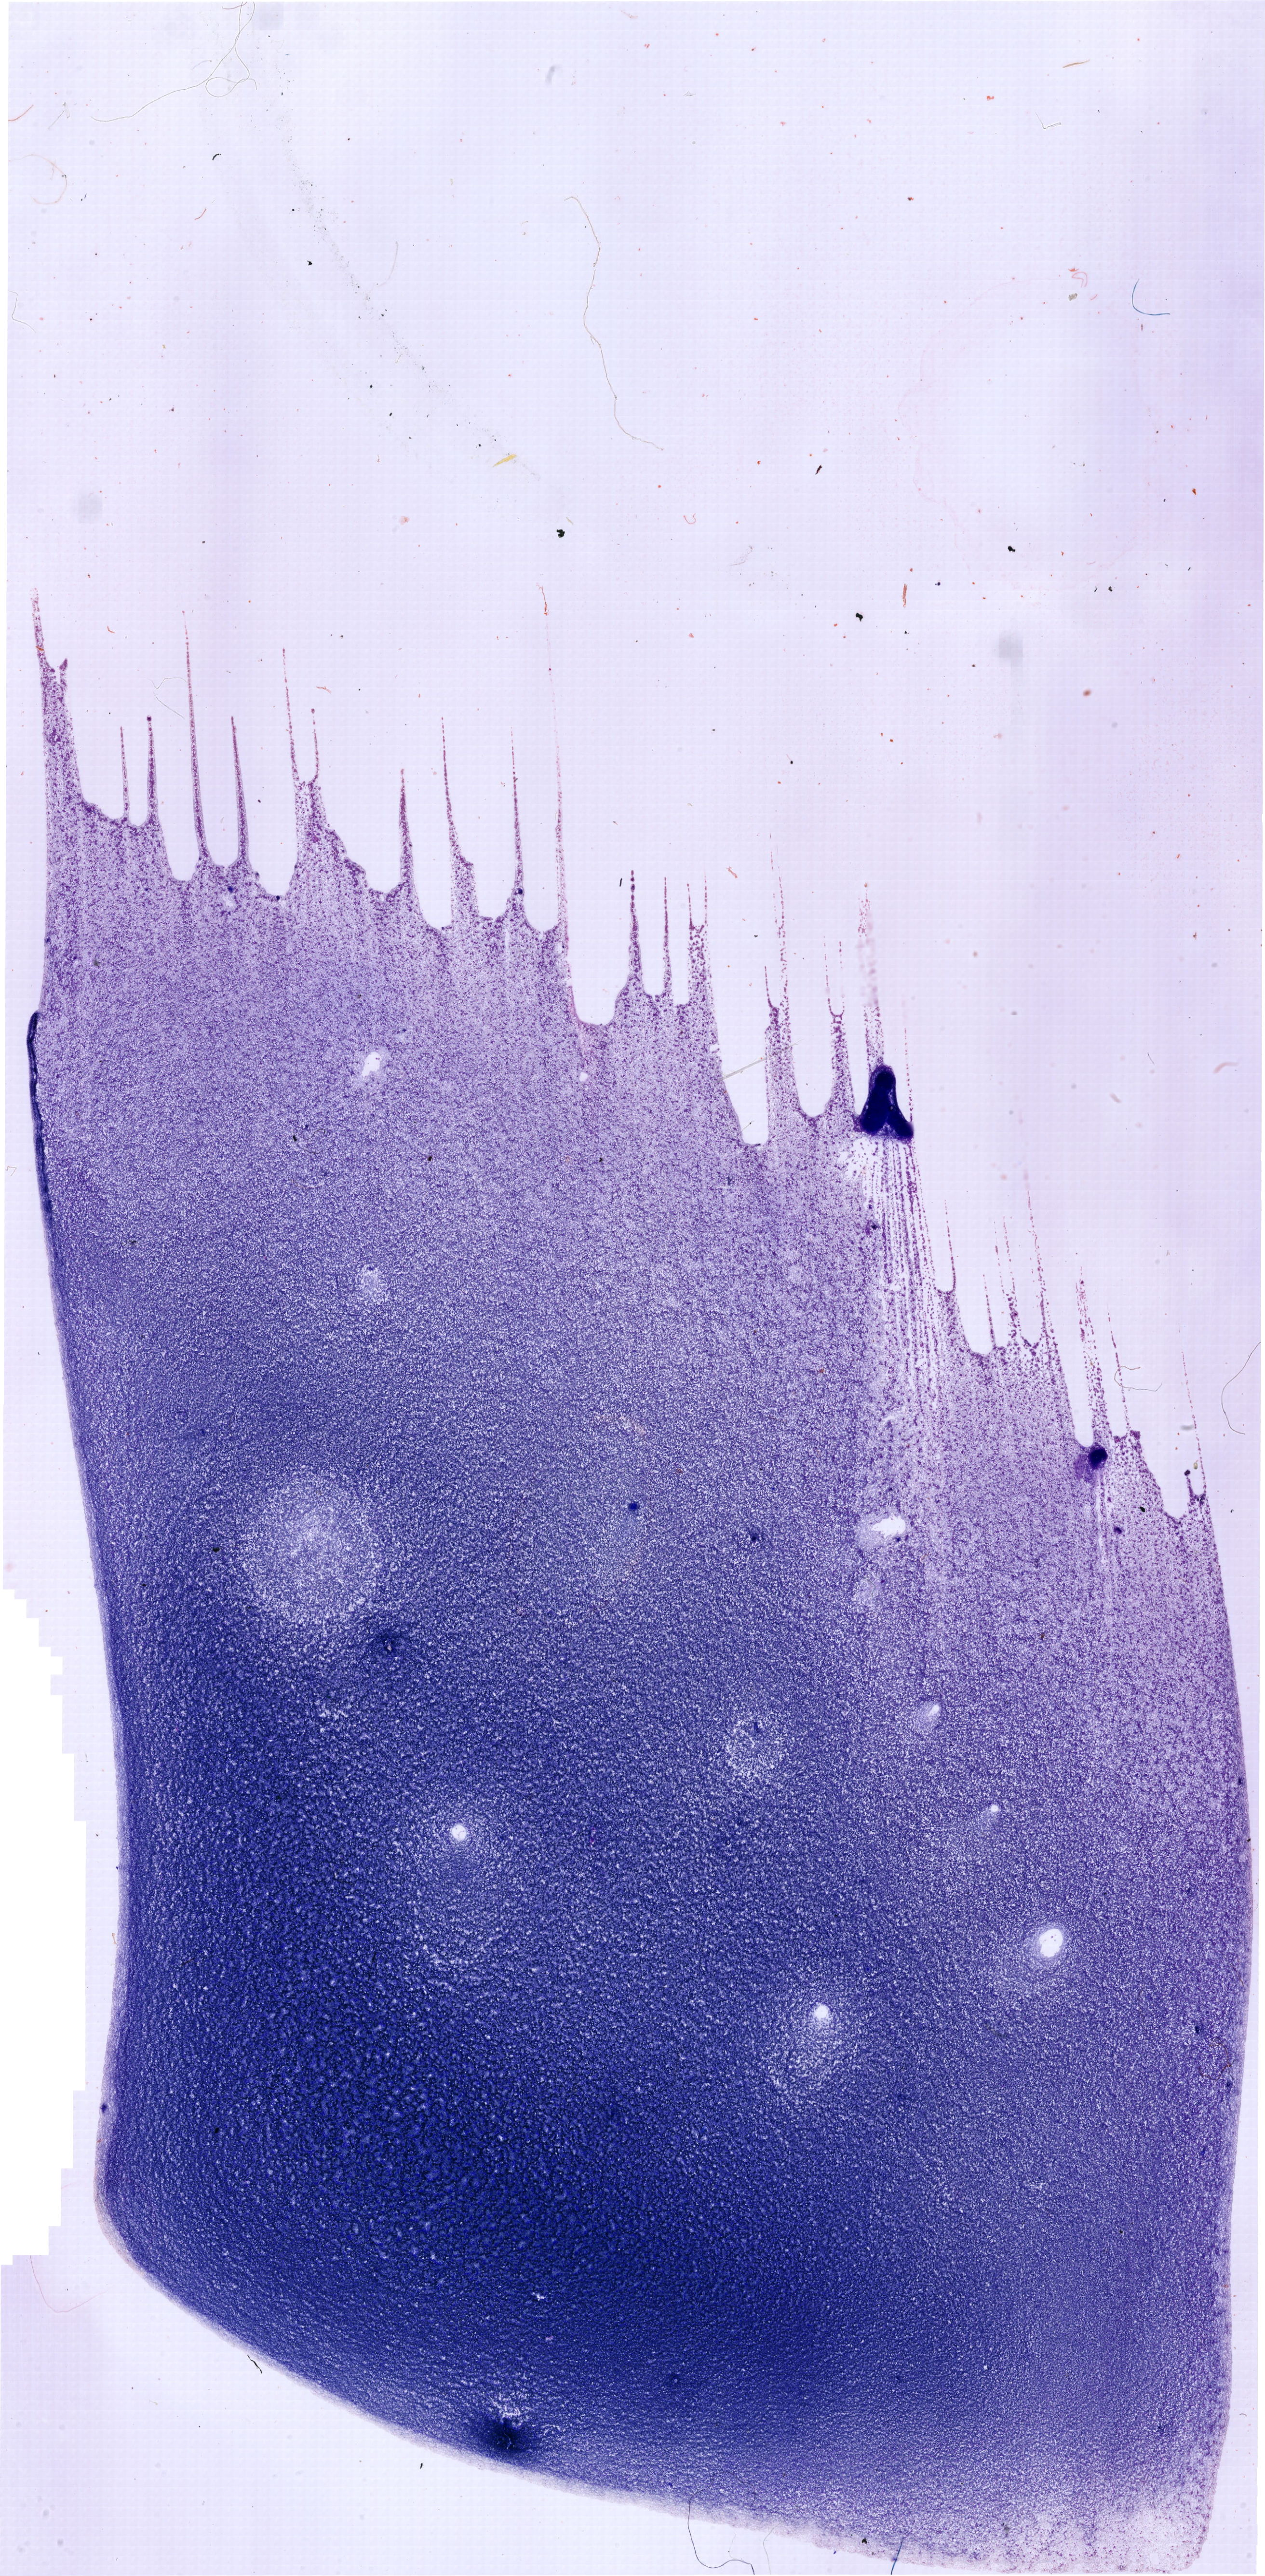
May-Grünwald–Giemsa-stained marrow aspirate smear (whole slide), a low-resolution overview of the entire scanned area, about 20.5 x 41.7 mm. Male patient.
Diagnosis: T Acute Lymphoblastic Leukemia.